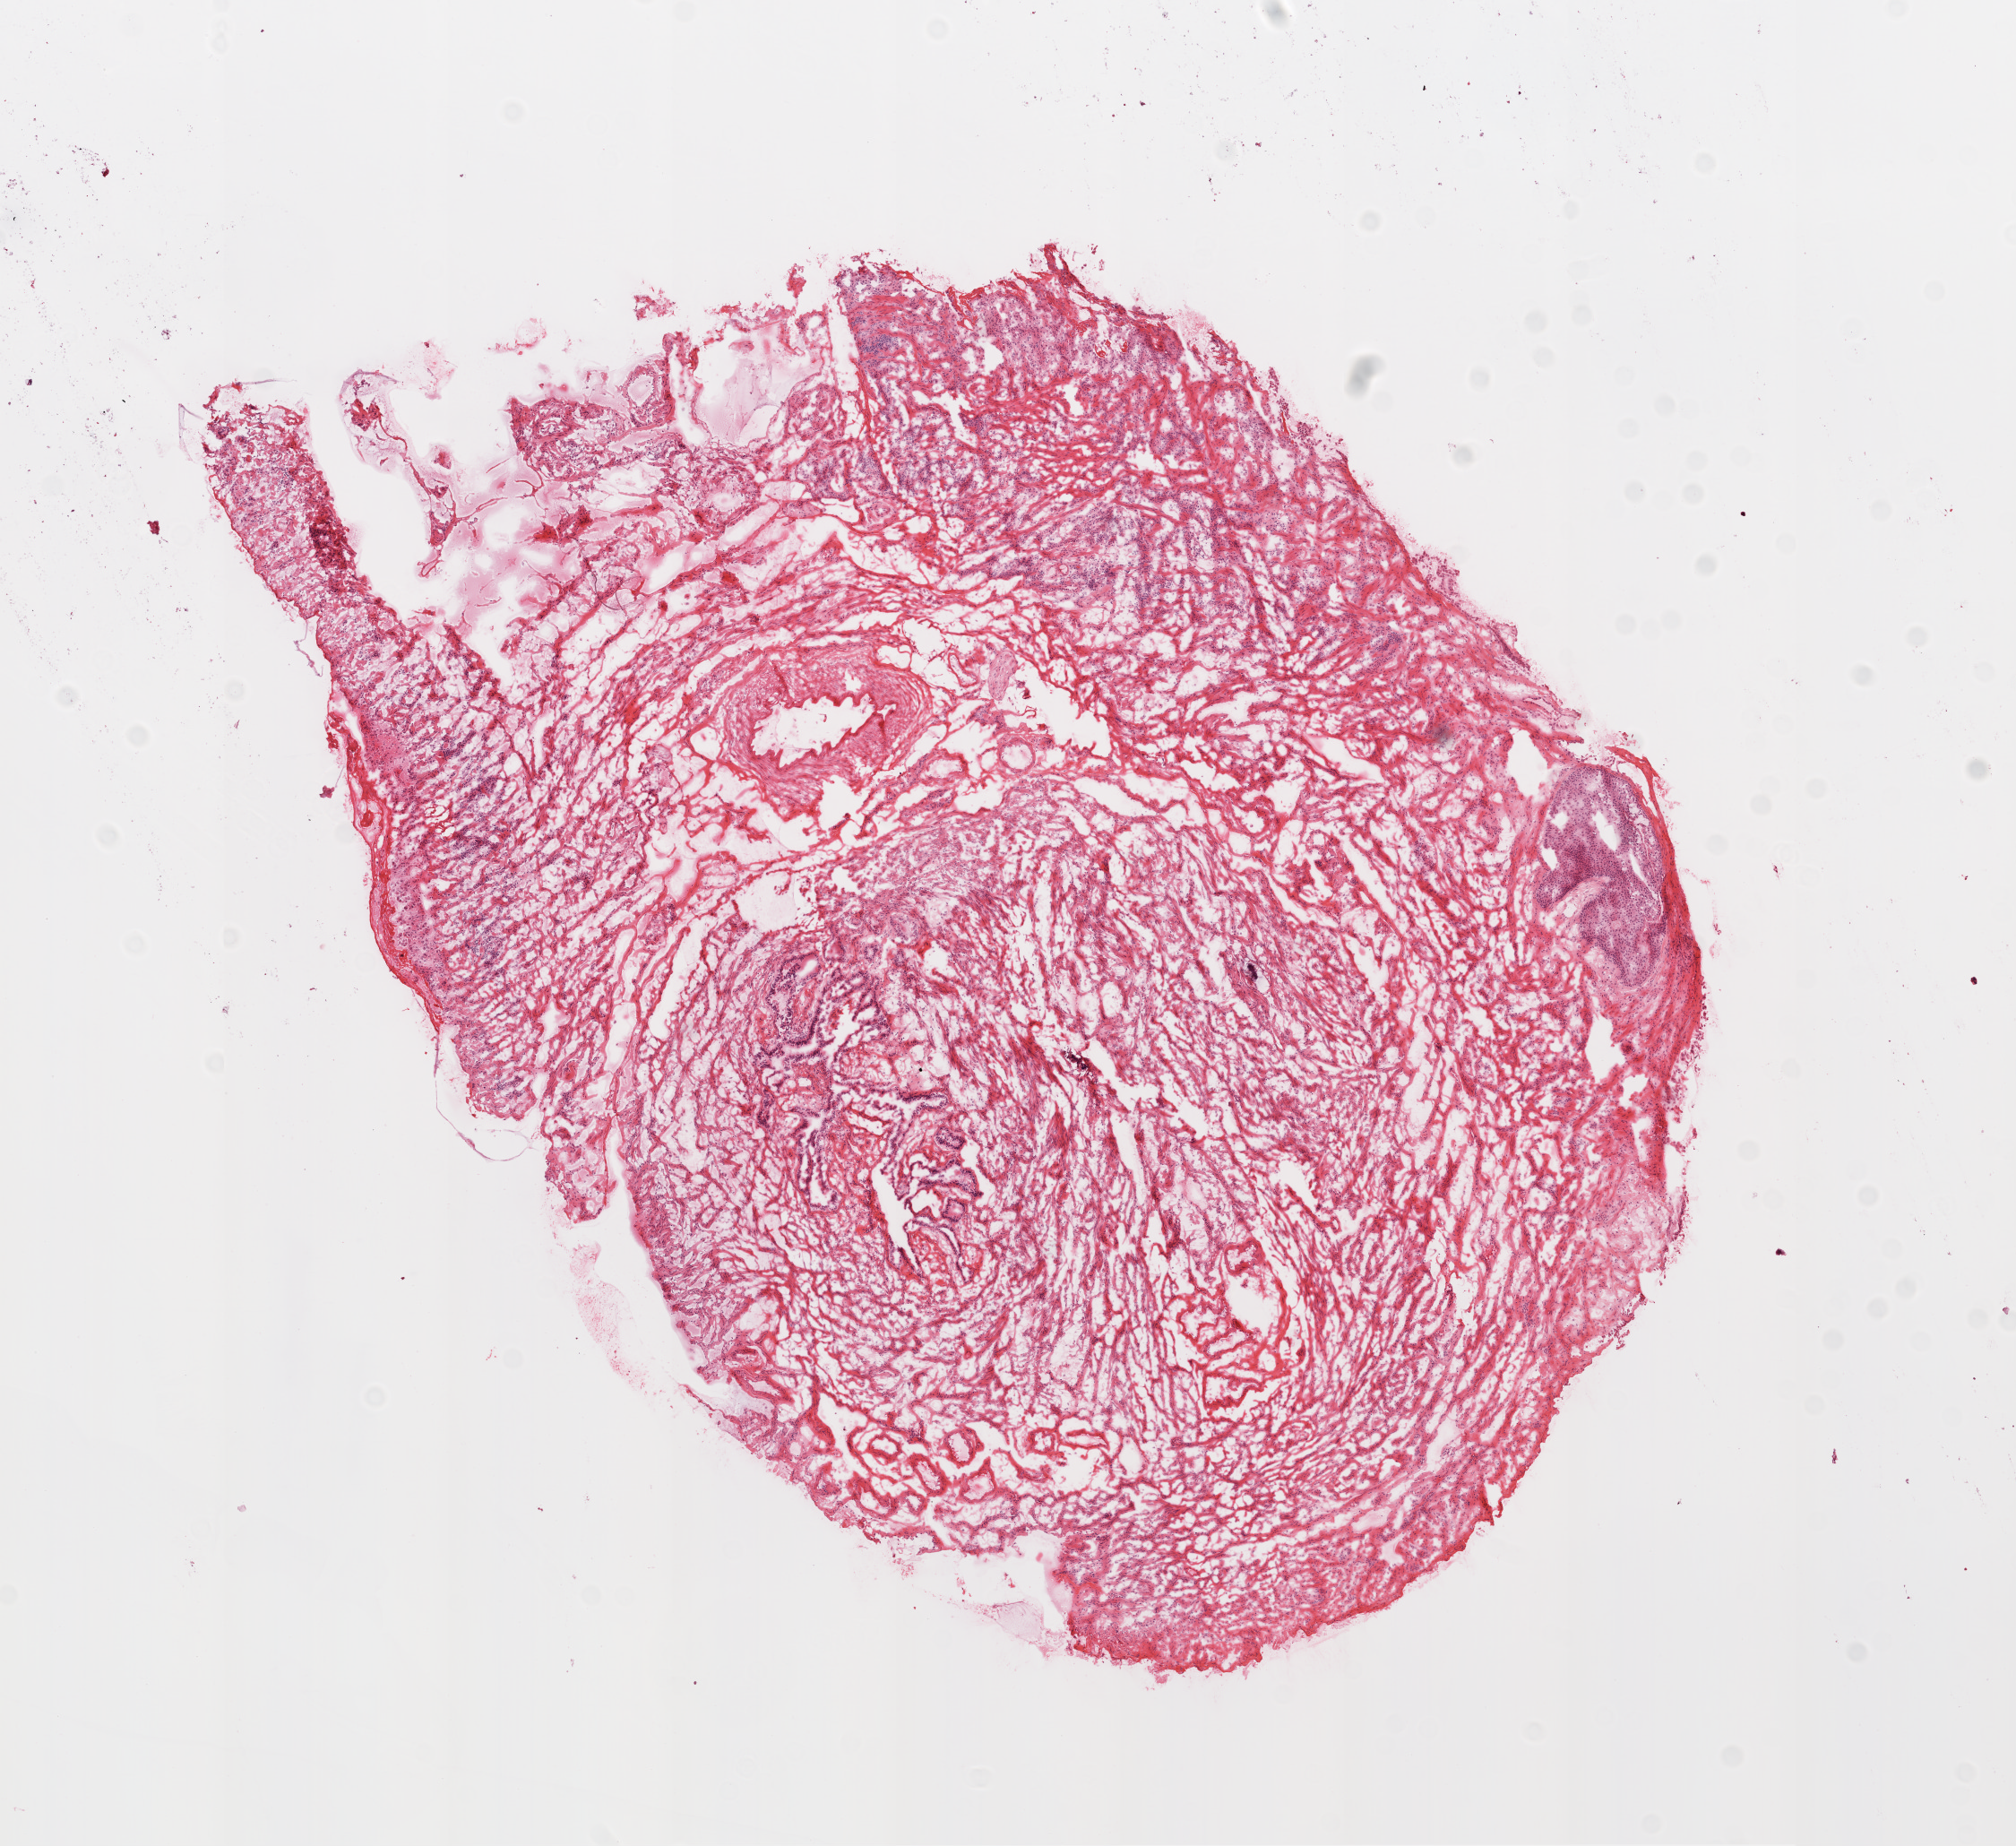
Digitized Hematoxylin and eosin (H&E) stained tissue section (whole slide) — low-resolution overview of the scanned area, about 9.0 x 8.3 mm (acquisition: 20x scan); frozen section from the top of the tissue portion; solid tissue normal (non-tumour tissue) sample from the ovary. Patient: female, age at initial diagnosis 51 years.
• this section: solid tissue normal sample (biorepository sample class)
• patient diagnosis: Serous cystadenocarcinoma, NOS